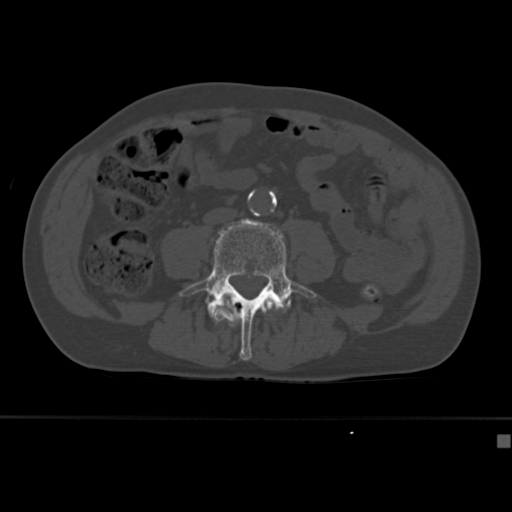
CT including the spine, one axial slice. 120 kVp. Bone window (W 1800 / L 400 HU). 512 × 512 image matrix. Male patient, age 64 years. From the clinical record (not read from this slice): primary cancer: uterus.
Outlined on this slice (semi-automatically segmented with operator editing):
- L3 vertebra: bounding box [x1, y1, x2, y2] px = [223, 295, 274, 311]
- L4 vertebra: [179, 218, 317, 360]